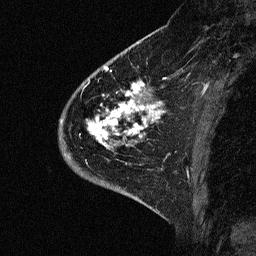
Breast MRI (dynamic contrast-enhanced), one sagittal slice. Position 18 of 64 along the scan axis. Dynamic contrast-enhanced study with each time point stored as its own series, time point 2 of 3 at this slice position (early post-contrast, ordered by acquisition time). 1.5 T. TE 4.5 ms, TR 11 ms. 2.06 mm slice thickness. 256 × 256 image matrix, field of view 200 × 200 mm. Female patient, age 46 years. Case-level facts recorded for this patient, not image findings: setting: breast cancer imaged before/during neoadjuvant chemotherapy; receptor status: HER2-positive.
Outlined on this slice (semi-automatically segmented with operator editing):
- analysis volume of interest (the breast-tissue region the enhancement analysis was run in; not a lesion): bounding box (x1, y1, x2, y2) in pixels: (43, 72, 176, 177)
- tumour enhancement mask (voxels above the 90 % enhancement threshold inside the analysis volume of interest): (79, 78, 166, 163)